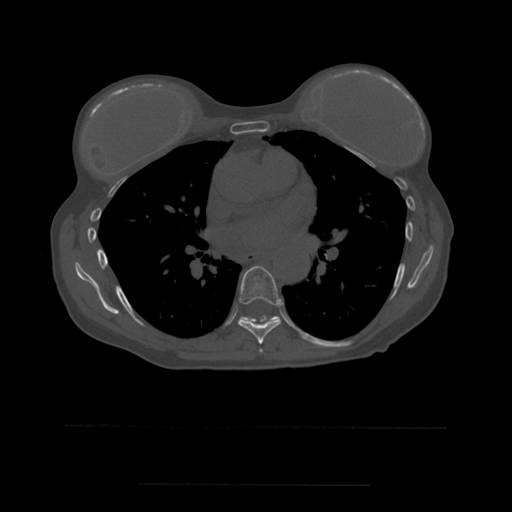
CT including the spine, one axial slice; bone window (W 1800 / L 400 HU); 1.25 mm slice thickness; 512 × 512 image matrix, field of view 350 × 350 mm. Patient age 58 years. From the clinical record (not read from this slice): primary cancer: lung.
Structures marked on this image (semi-automatic segmentation, software-assisted and operator-edited):
- T6 vertebra: bounding box <260,349,263,353> (left, top, right, bottom; pixels)
- T7 vertebra: <238,266,282,344>
- T8 vertebra: <240,317,274,323>